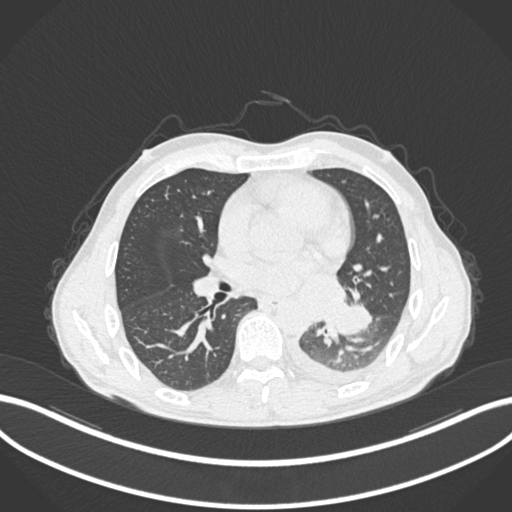
Chest CT, one axial slice; position 118 of 222 along the scan axis; reconstruction kernel B30f; 120 kVp; lung window (W 1500 / L -600 HU); 1 mm slice thickness; 512 × 512 image matrix, field of view 400 × 400 mm. Male patient, age 47 years. Case-level facts recorded for this patient, not image findings: clinical TNM (as recorded): T3 N1 M1c.
Annotated regions visible in this slice (rectangle marked by the reading radiologist):
- lung tumour (recorded histology: small cell carcinoma): bounding box (x1, y1, x2, y2) in pixels: (324, 302, 377, 342)